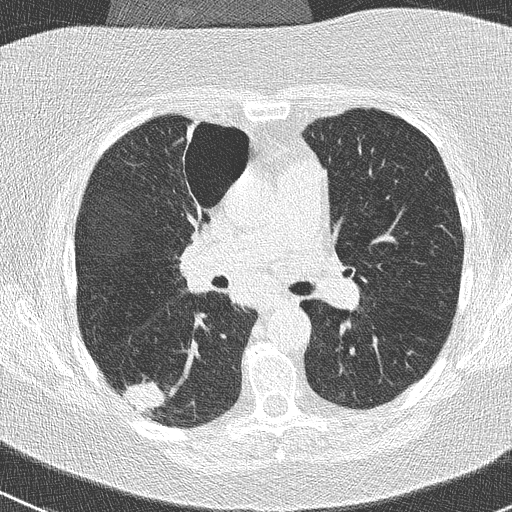
Chest CT (low-dose screening protocol), one axial image; first (baseline) screen; lung window (W 1500 / L -600 HU); 2 mm slice thickness; lung (sharp) reconstruction kernel (B50f); slice 109 of 261 in the series; 512 × 512 image matrix, field of view 310 × 310 mm. Female, age 74 years at enrolment. Former smoker at enrolment.
- Expert-annotated lung lesion, bounding box [x1, y1, x2, y2] px = [117, 377, 174, 425].
- The screening reader recorded 3 non-calcified nodules or masses ≥4 mm on this exam (right lower lobe, right upper lobe, left lower lobe); which of them this box marks is not recorded.
- Official screen result: positive, change unspecified: nodule(s) >= 4 mm or enlarging nodule(s), mass(es), or other non-specific abnormalities suspicious for lung cancer.
- Participant outcome: lung cancer diagnosed 16 days after this screen — non-small cell carcinoma, right lower lobe, poorly differentiated (G3), stage IIIA (AJCC 6th edition), 28 mm at pathology.